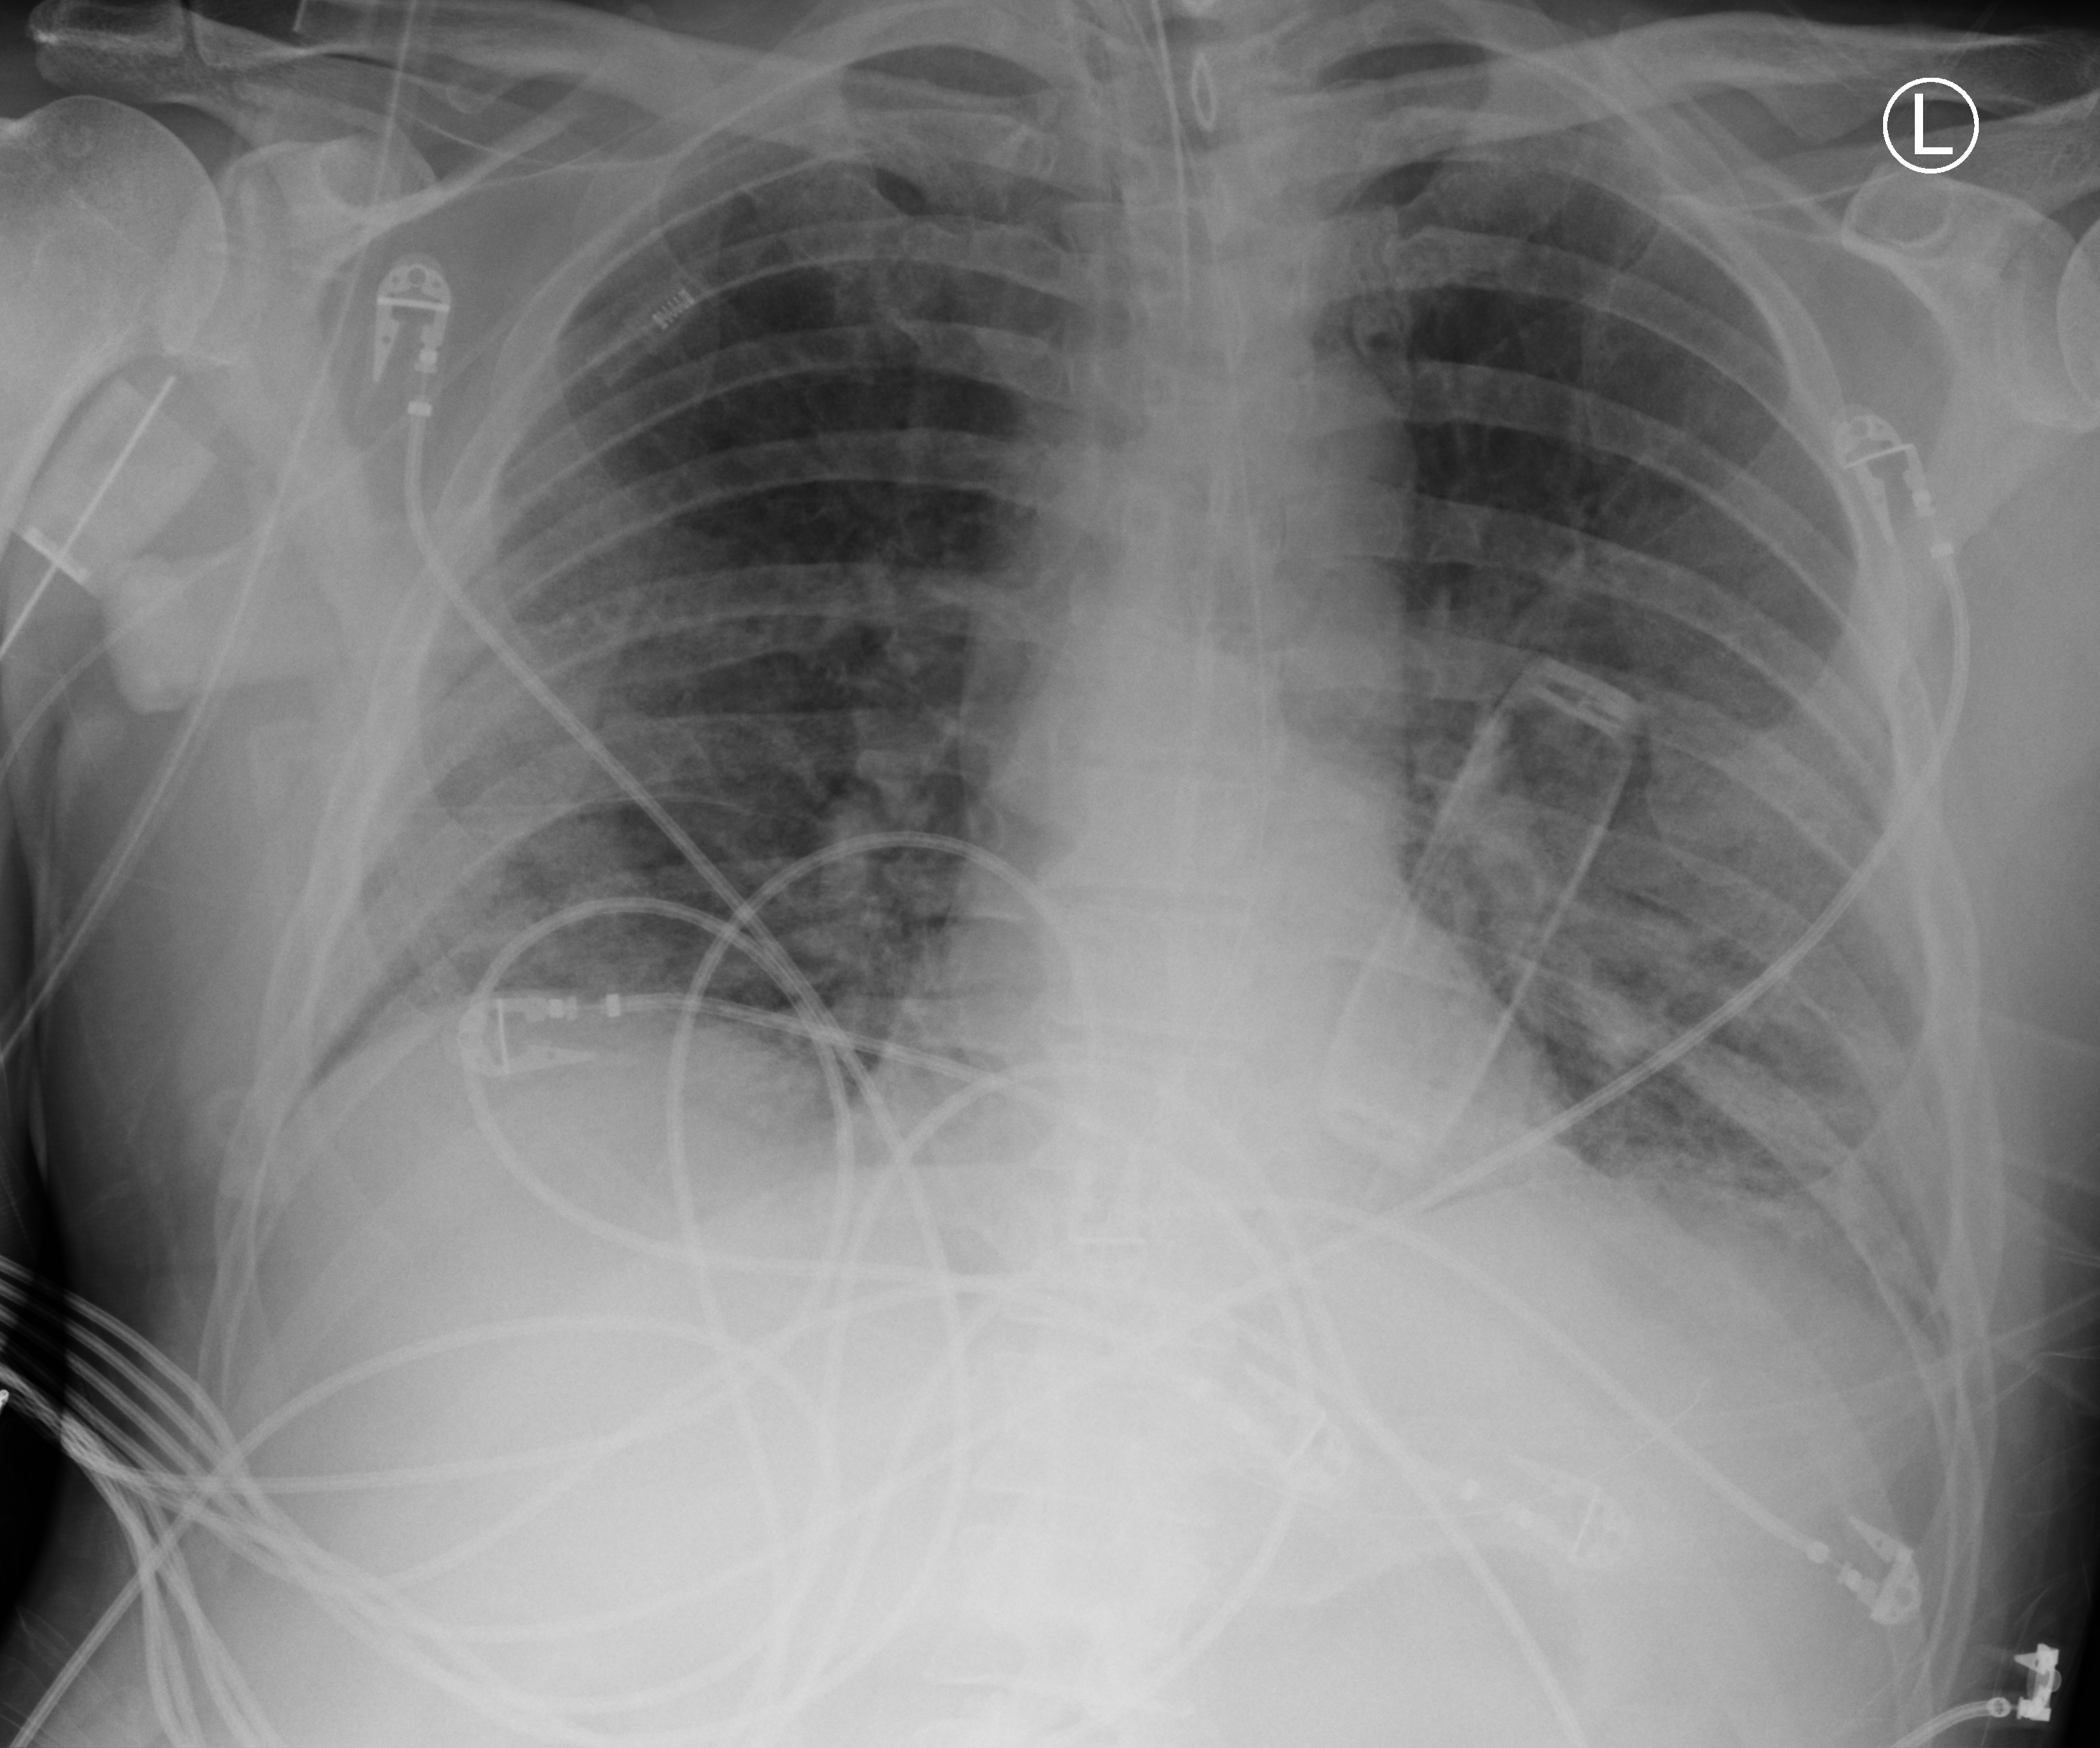
Portable chest radiograph; anteroposterior (AP) projection. Male patient hospitalised with COVID-19, age 60–74 years.
Admission-level facts for this patient (not findings on this image; timing relative to this image not recorded):
- chronic kidney disease (admission record): no